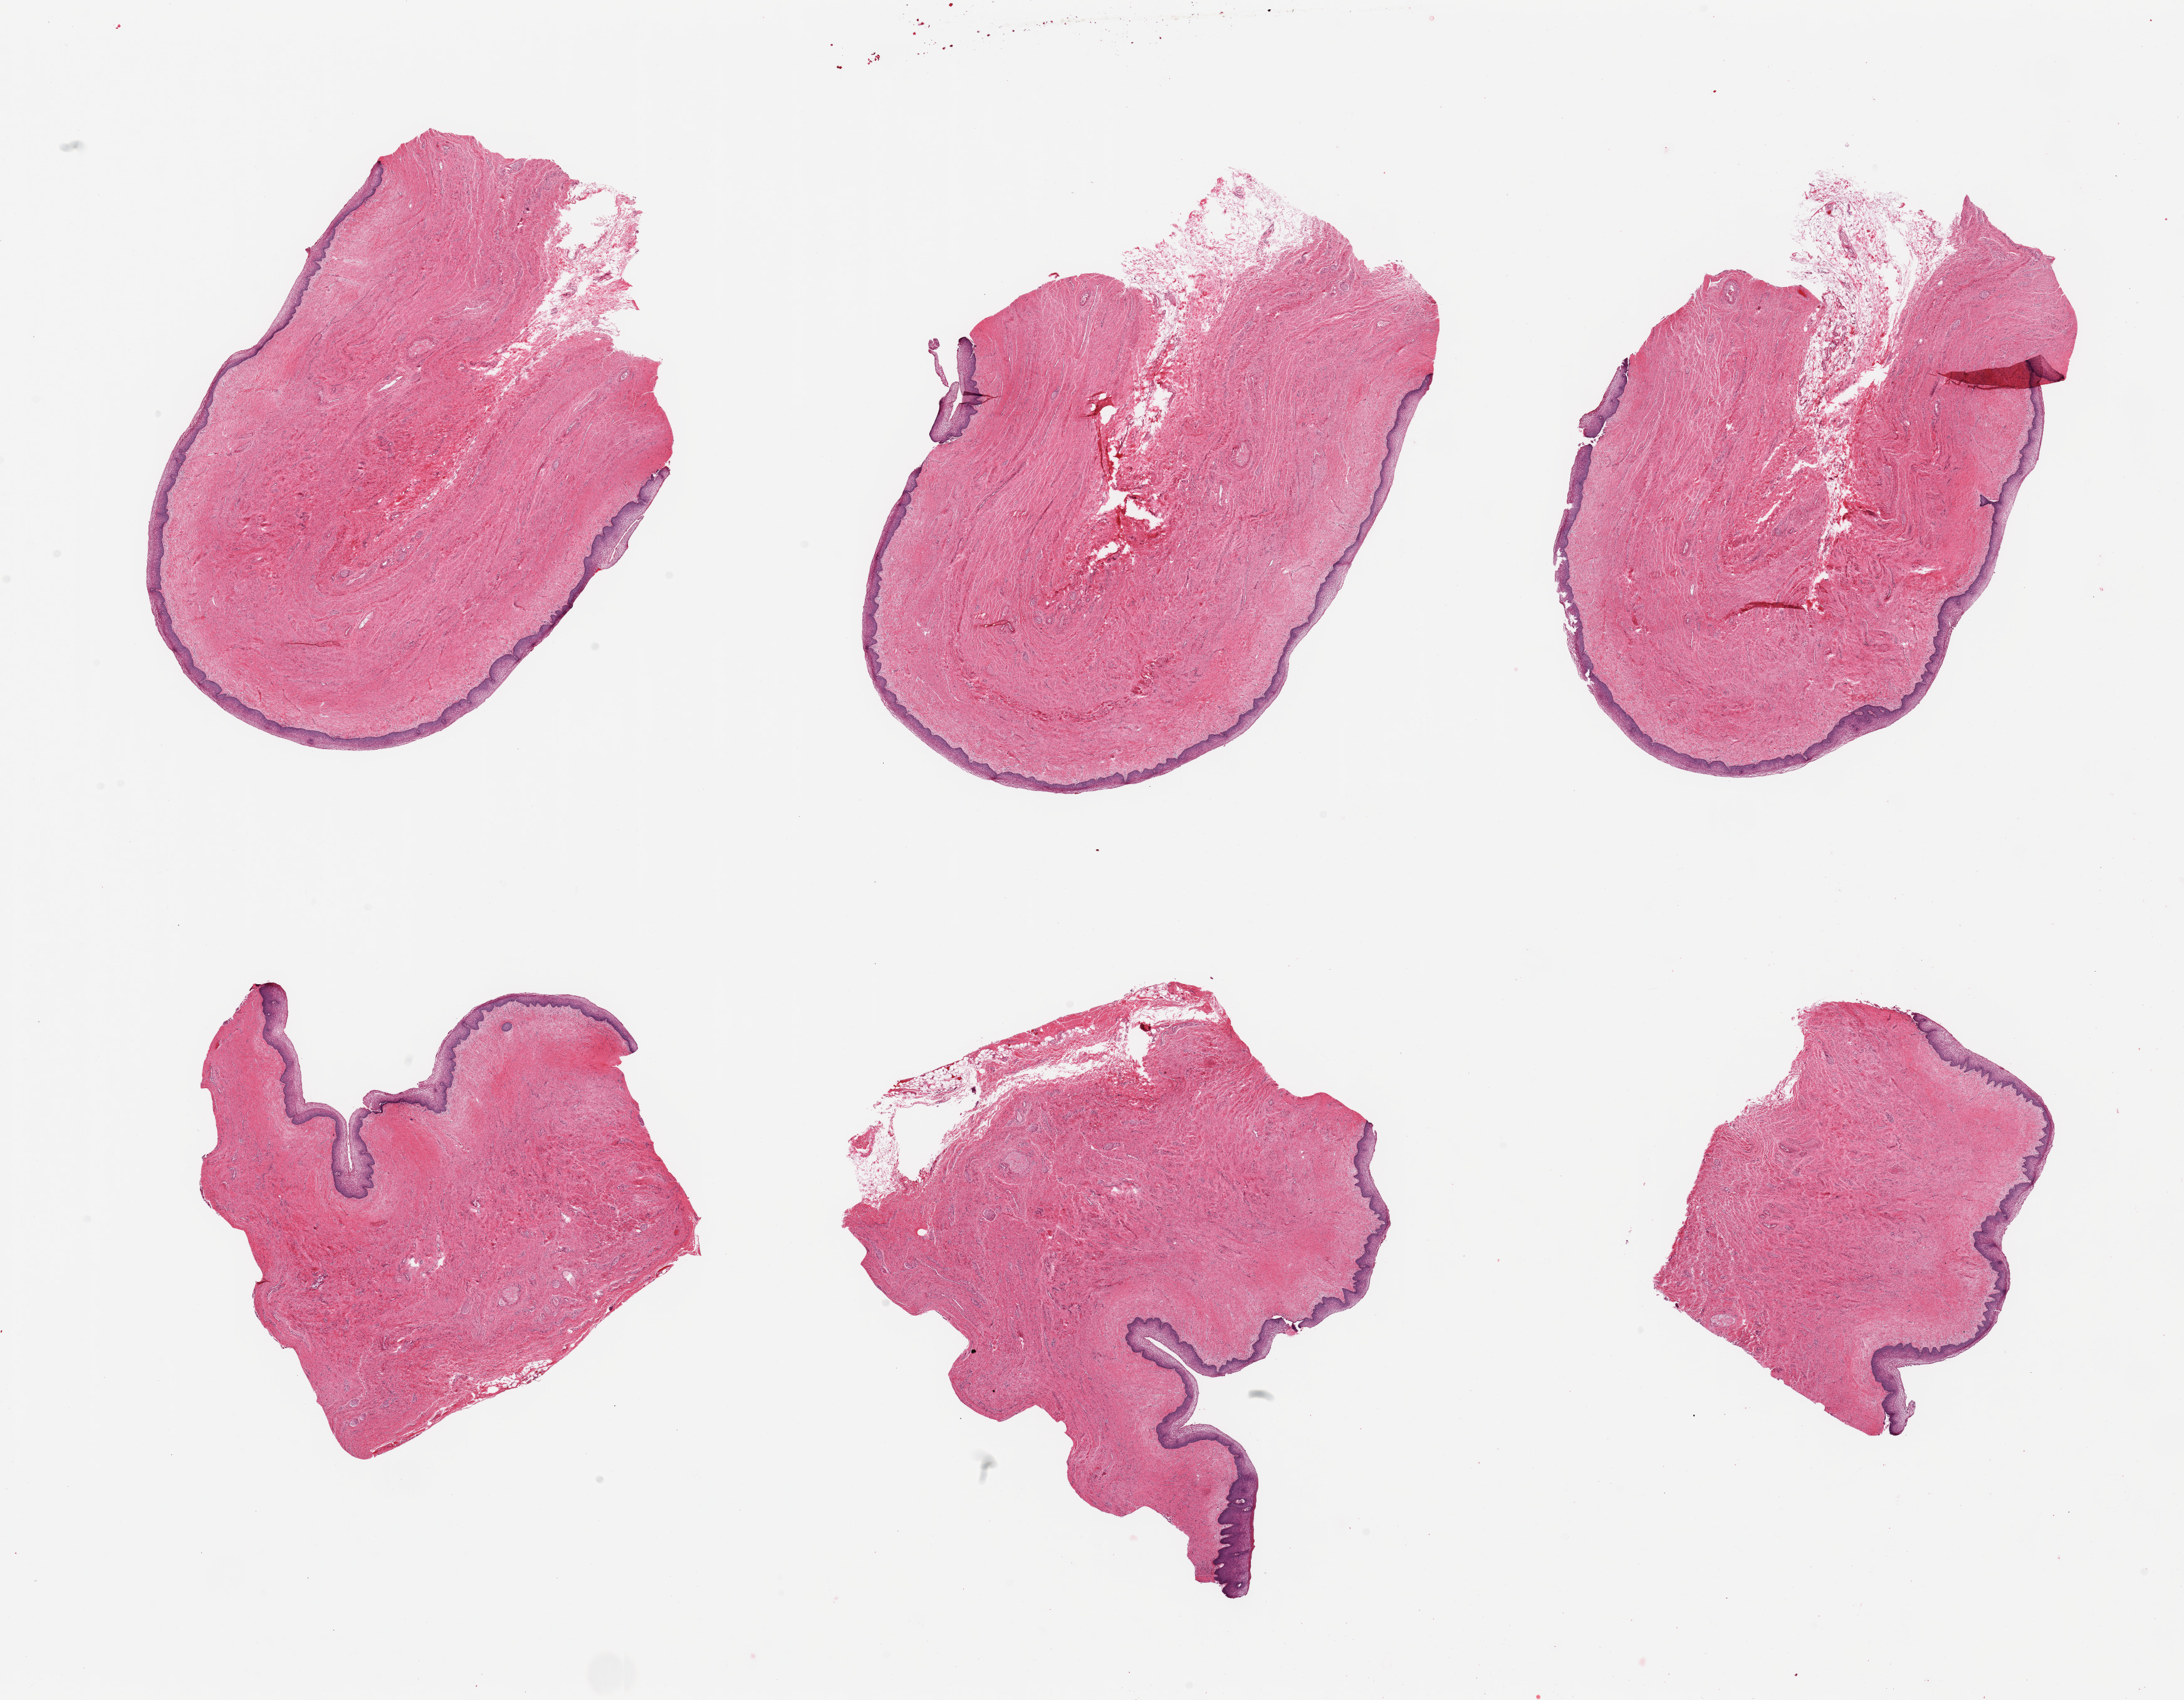
Hematoxylin and eosin (H&E) whole-slide image — shown as a low-resolution overview of the whole scanned area (about 27.6 x 21.5 mm). PAXgene-fixed paraffin-embedded (PFPE) section. Target tissue: vagina. Donor tissue sample. Donor sex: female.
Review note (as recorded): 6 pieces; squamous mucosa present on all pieces.